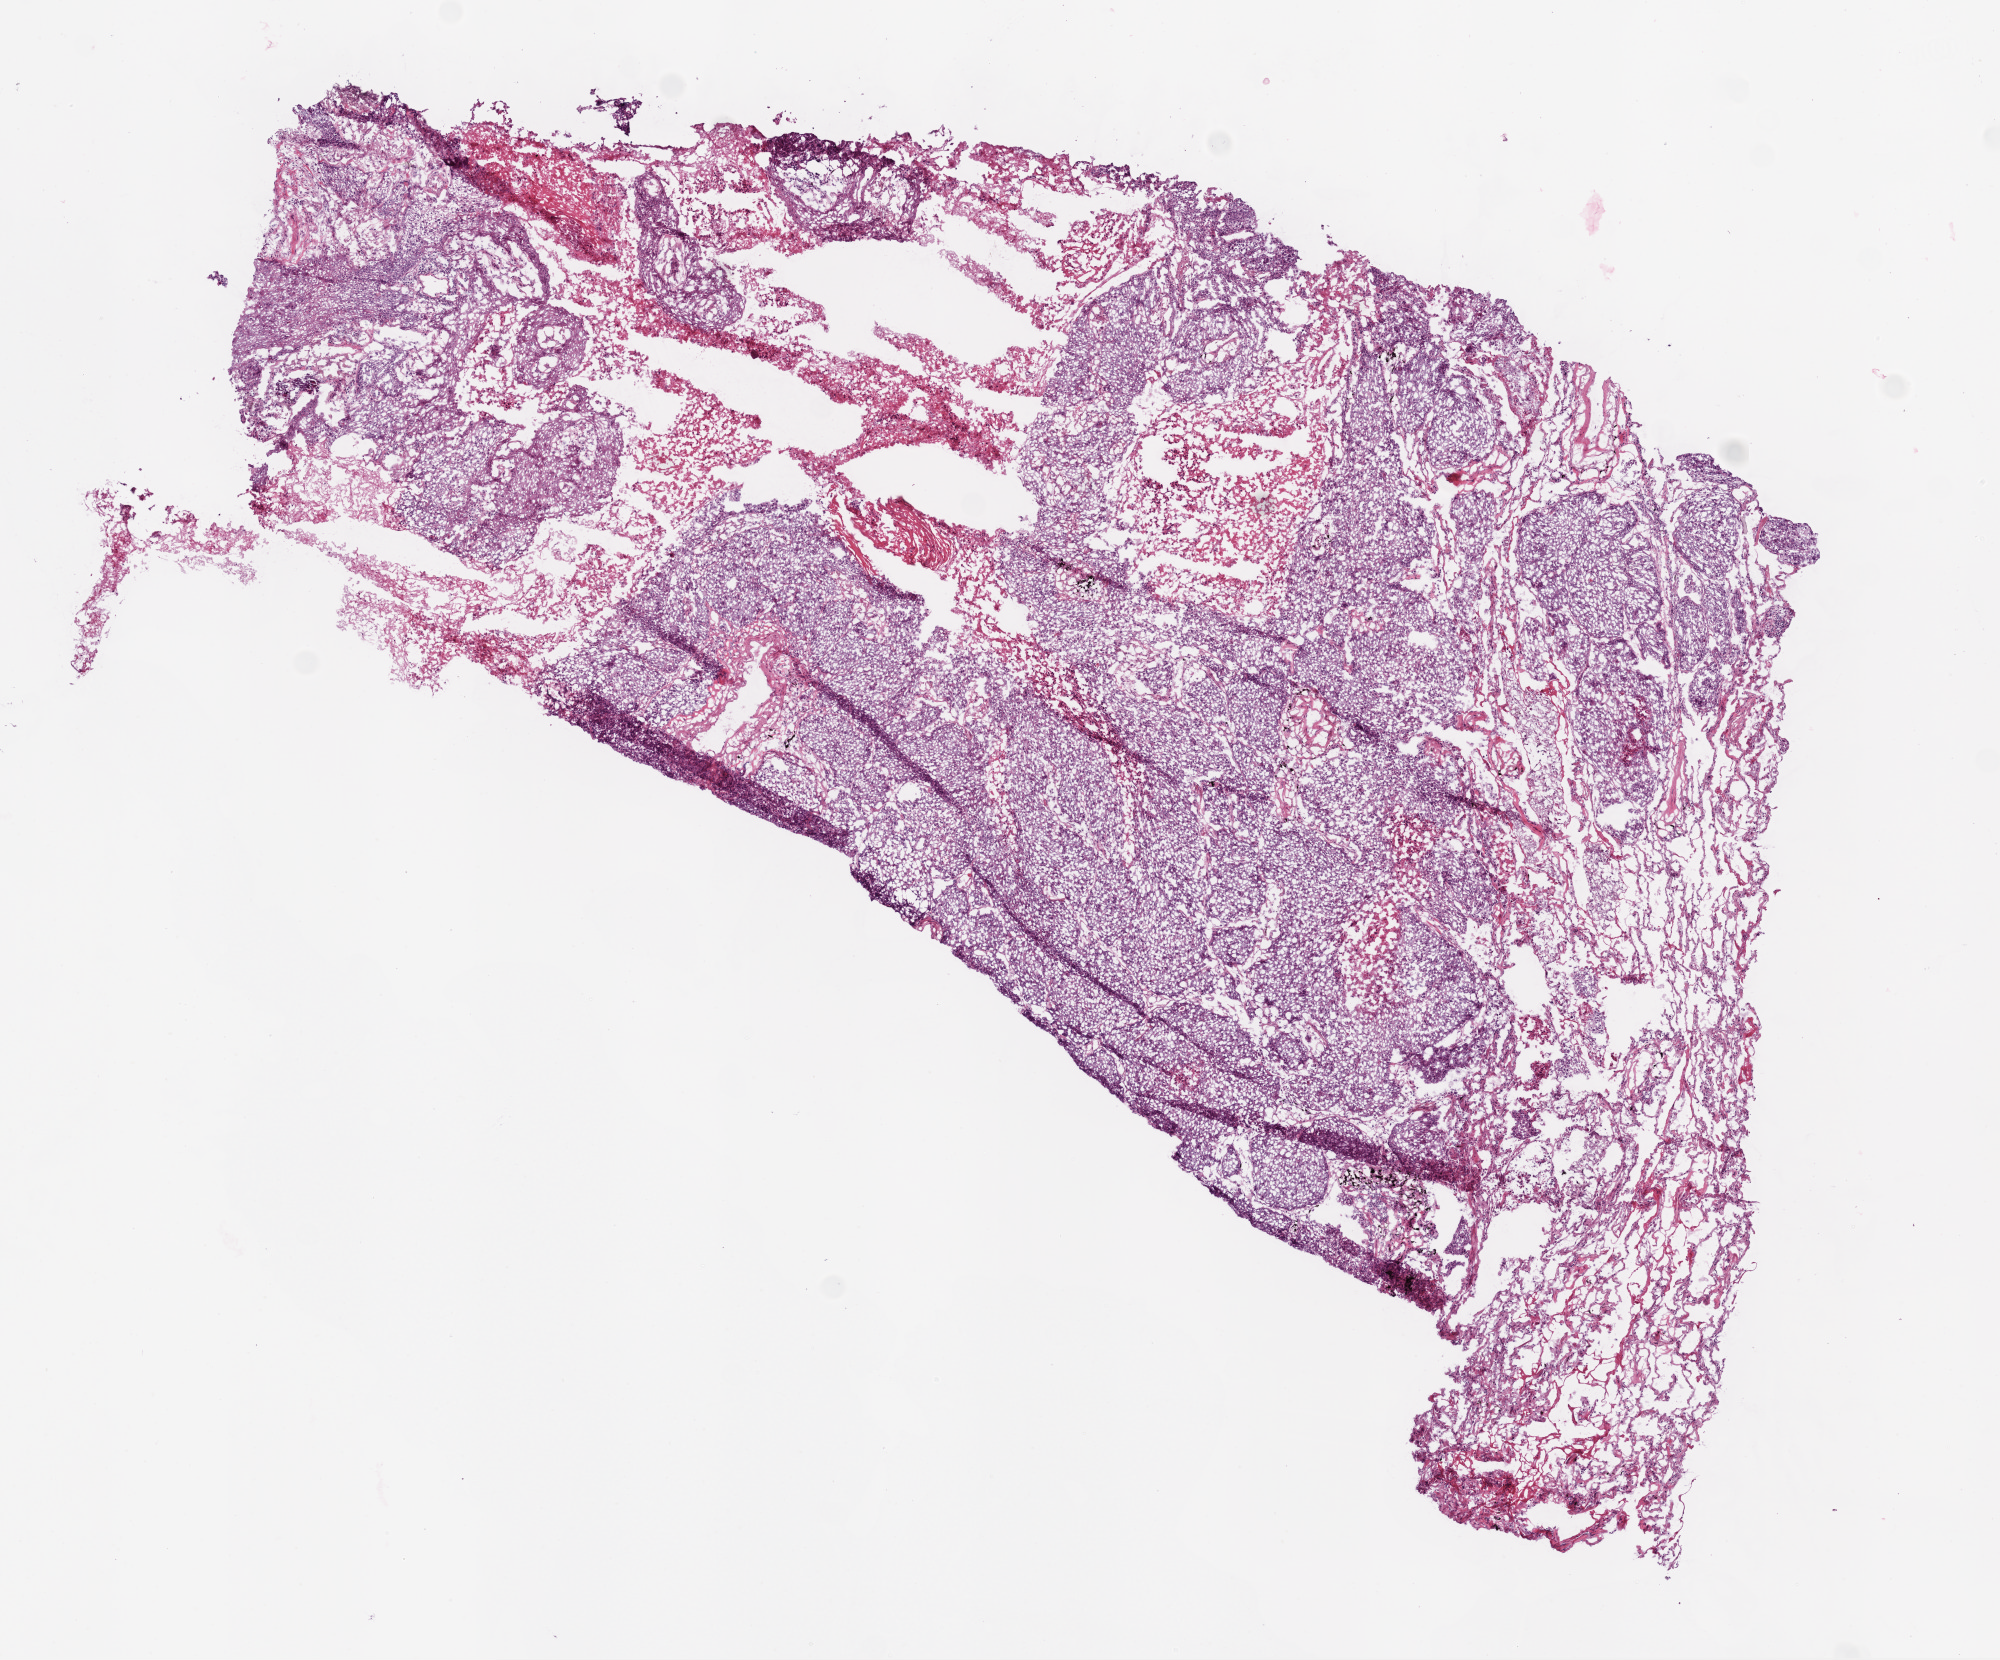
Whole-slide histology image, Hematoxylin and eosin (H&E) stained — whole scanned area (about 8.0 x 6.7 mm) shown as a low-resolution overview. Frozen section from the bottom of the tissue portion. Sample: primary tumour, lung. Female, age 76 years at initial diagnosis. Pathologist review of this section (percent, as recorded): tumour cells 75%, tumour nuclei 90%, normal cells 0%, stromal cells 10%, necrosis 15%.
Histologic diagnosis: Squamous cell carcinoma, NOS (lower lobe, lung). Laterality: right. AJCC pathologic stage: IA.